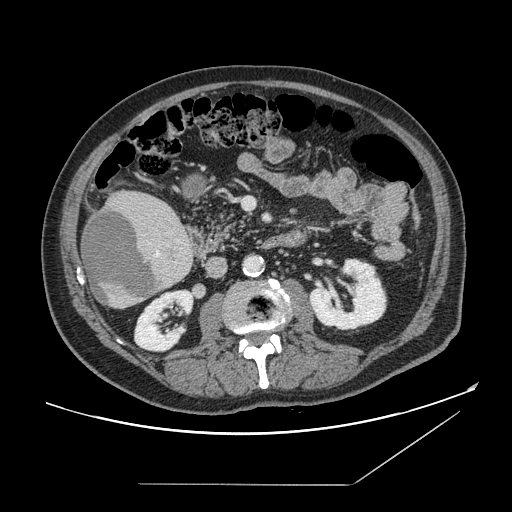
Contrast-enhanced abdominal CT, one axial slice. Slice 57 of 166 in the series (ordered by position). Intravenous contrast given. Soft-tissue window (W 400 / L 40 HU). 512 × 512 image matrix. Male patient, age 80 years. From the clinical record (not read from this slice): diagnosis: colorectal cancer liver metastases, imaged before liver resection; multiple liver metastases: no.
Structures marked on this image (outlined manually by an expert reader):
- liver: bounding box (x1, y1, x2, y2) in pixels: (81, 191, 194, 309)
- planned liver remnant (the part of the liver to remain after resection): (144, 196, 161, 204)
- liver metastasis: (83, 209, 162, 304)